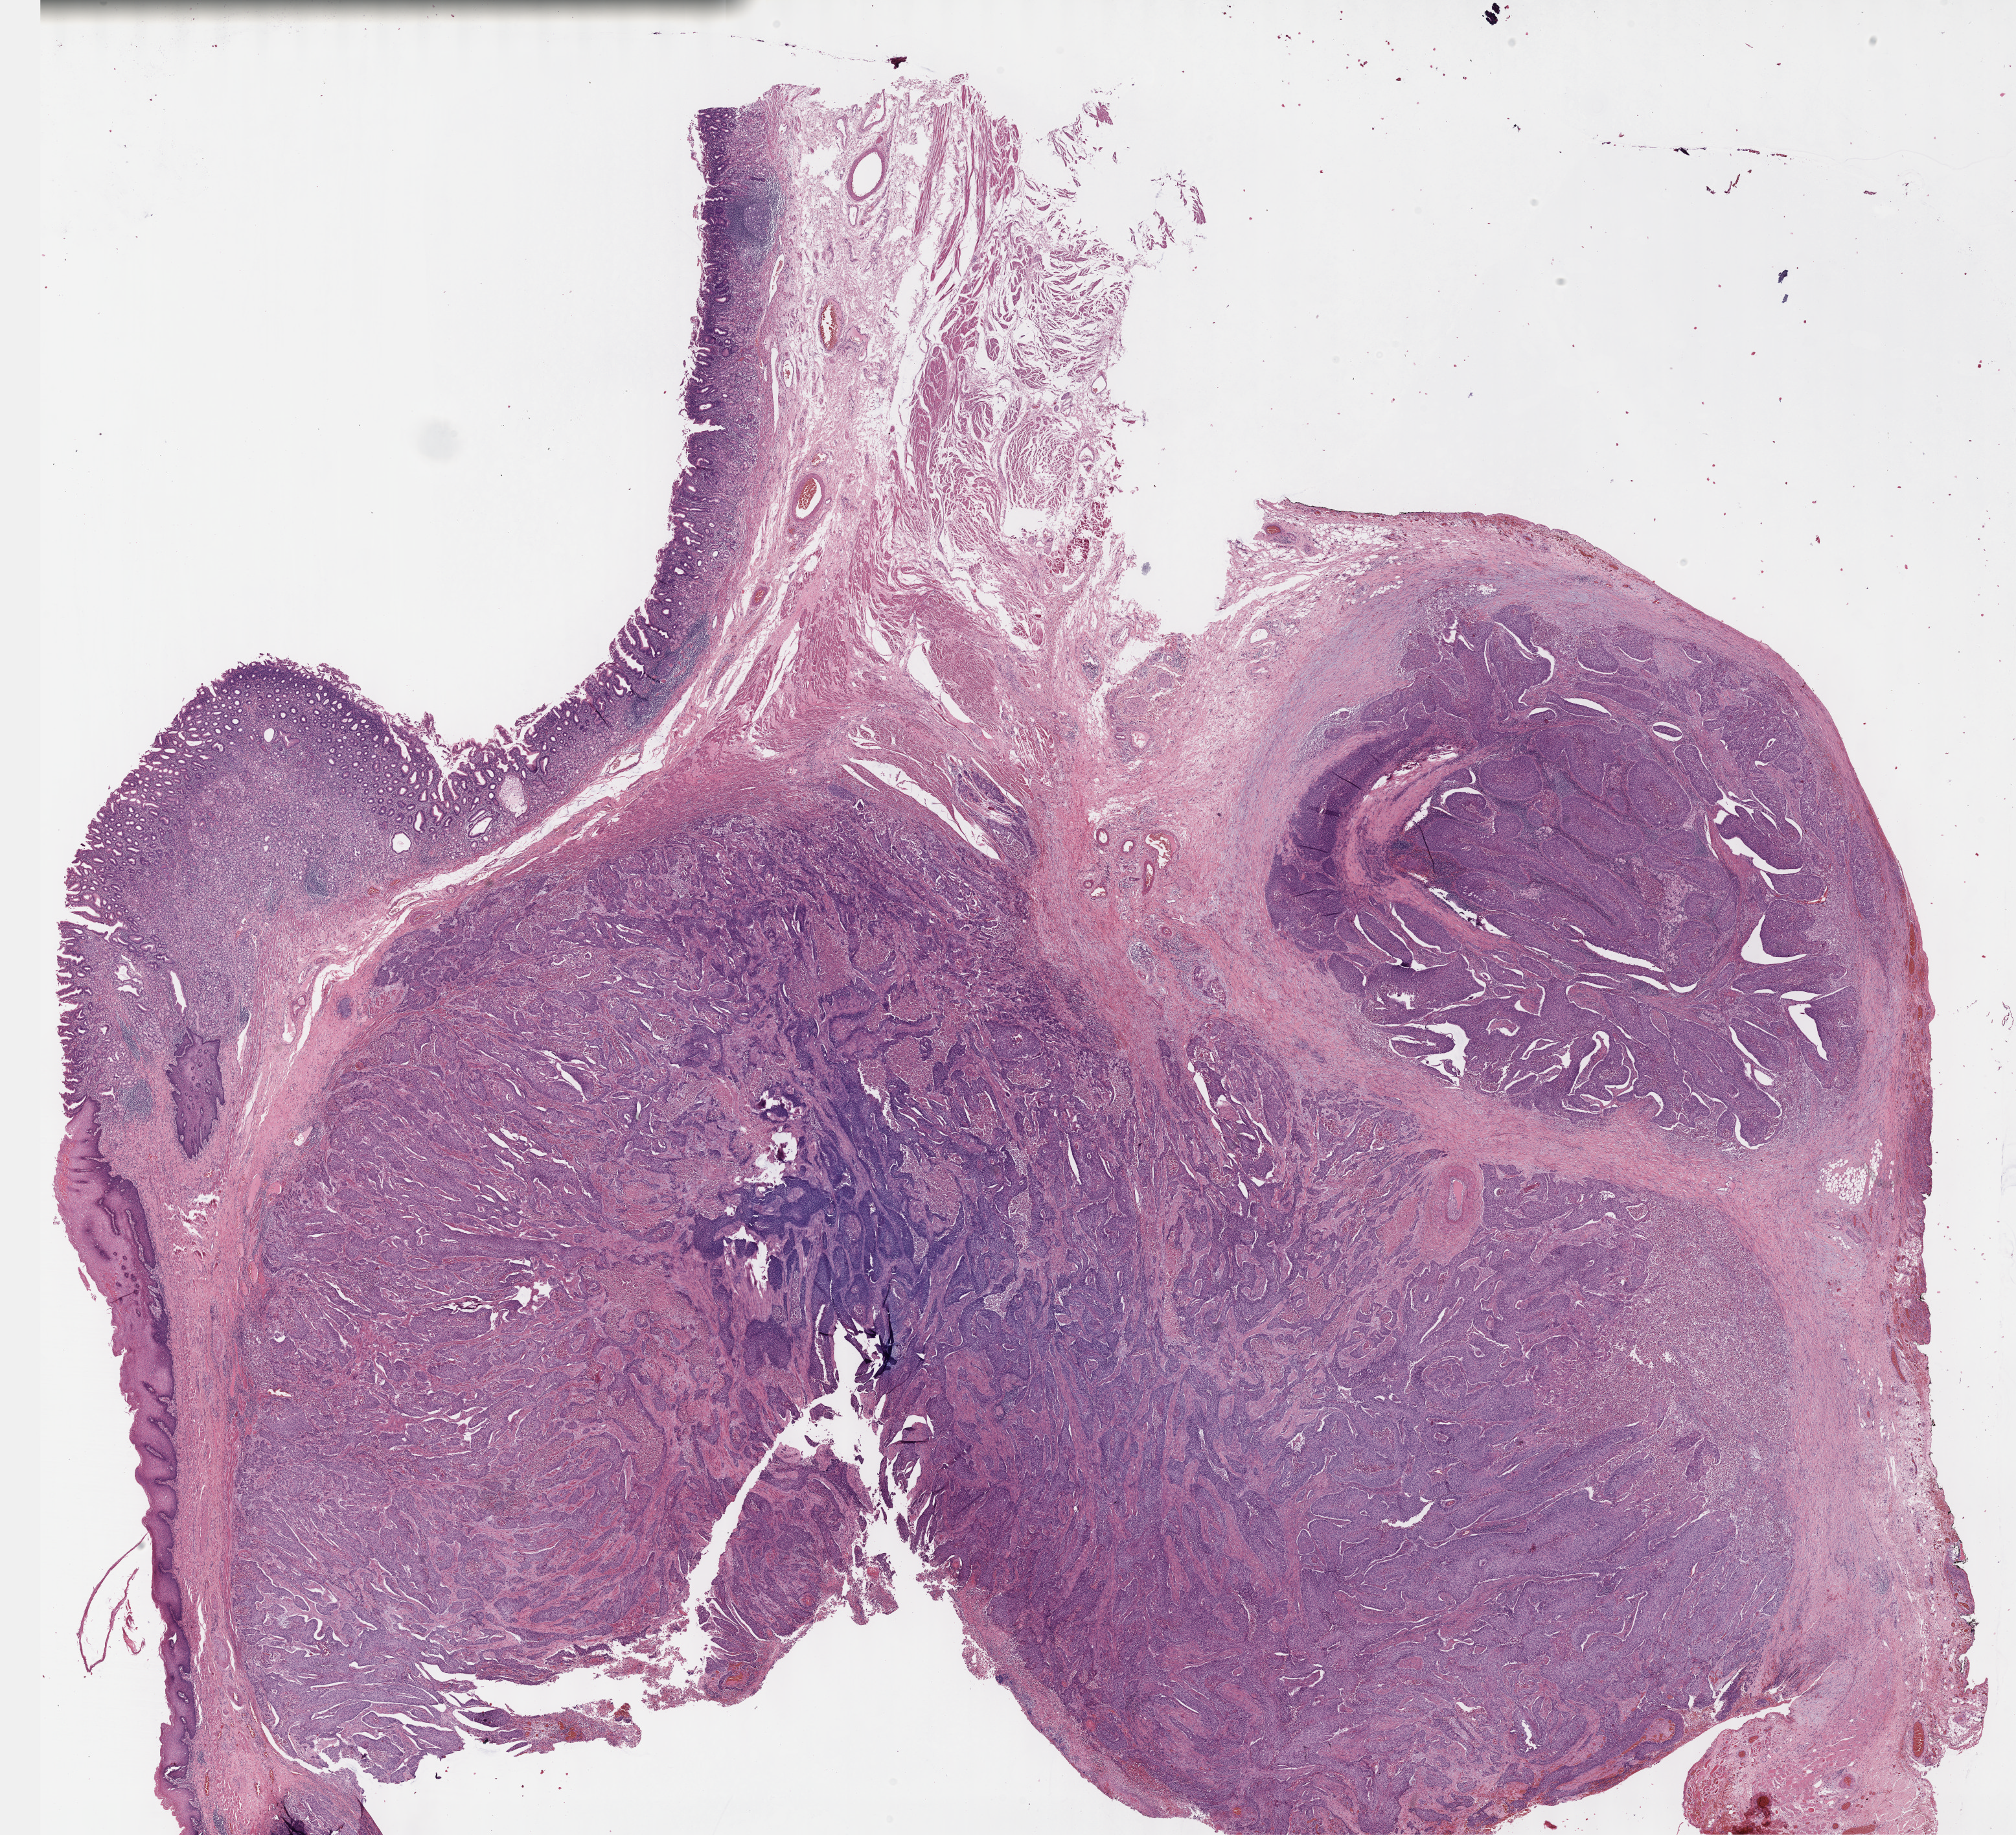
Whole-slide histology image, Hematoxylin and eosin (H&E) stained, low-resolution overview of the scanned area, about 25.1 x 22.9 mm. FFPE section. Esophagus, primary tumour sample. Patient: male, age at initial diagnosis 54 years. Histologic grade: GX (grade cannot be assessed).
Lymph nodes positive (case pathology): 3 of 14 examined. AJCC pathologic stage: III (6th edition). Diagnosis: Squamous cell carcinoma, NOS (lower third of esophagus).